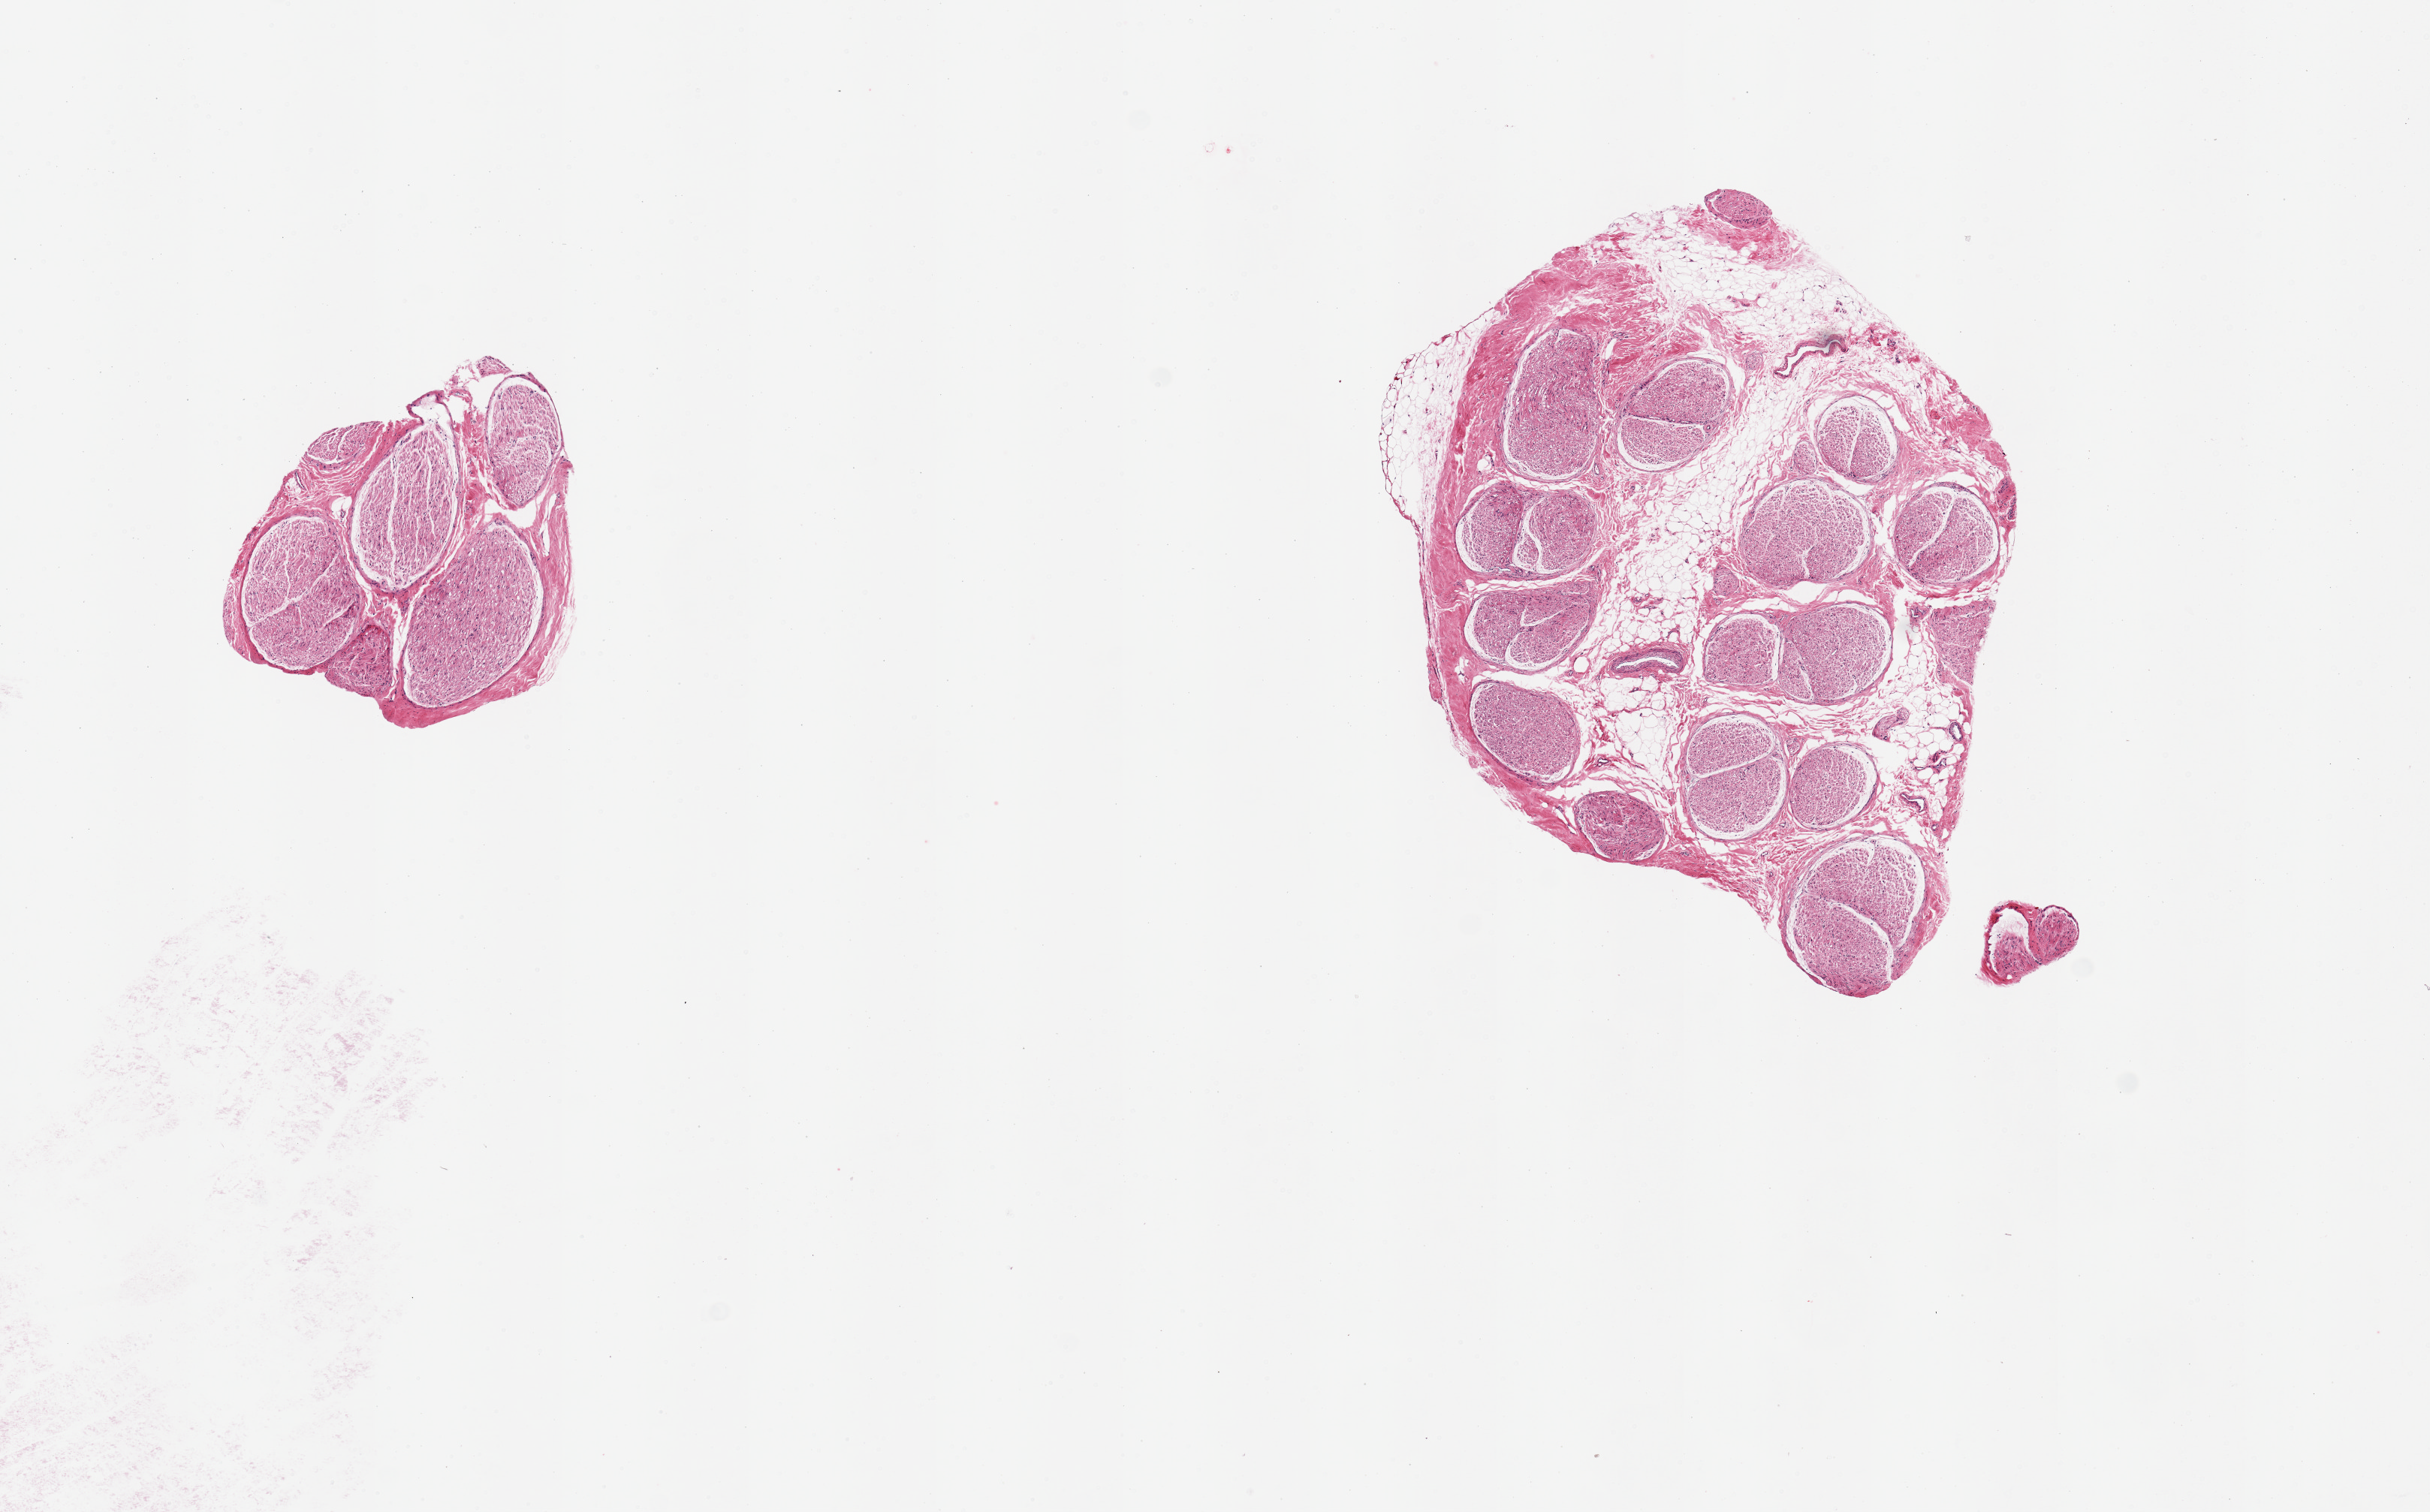
H&E whole-slide image, whole scanned area (about 12.8 x 8.0 mm) shown as a low-resolution overview; PAXgene-fixed paraffin-embedded (PFPE) section; sampled site (target tissue): tibial nerve; tissue donor sample.
* review note (as recorded): 2 pieces; 1 piece has 40% internal and external; fat; other is without extraneous fat